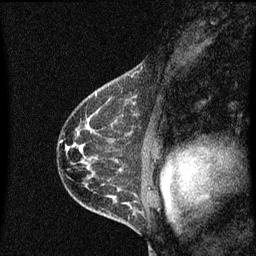
Breast MRI (dynamic contrast-enhanced), one sagittal slice. Position 44 of 60 along the scan axis. Dynamic contrast-enhanced series, image 2 of 3 at this slice position (ordered by acquisition). 1.5 T. TE 4.2 ms, TR 8.4 ms. 2 mm slice thickness. 256 × 256 image matrix, field of view 200 × 200 mm. Female patient, age 41 years.
Annotated regions visible in this slice (semi-automatically segmented with operator editing):
- analysis volume of interest (the breast-tissue region the enhancement analysis was run in; not a lesion): box from (x=121, y=74) to (x=142, y=99) px
- tumour enhancement mask (voxels above the 70 % enhancement threshold inside the analysis volume of interest): (x=133, y=74)–(x=135, y=77)